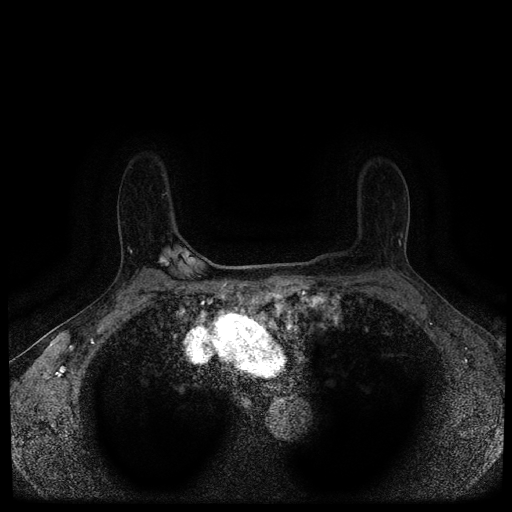
Breast MRI (dynamic contrast-enhanced, multi-phase), one axial slice. Position 77 of 116 along the scan axis. Dynamic contrast-enhanced series, time point 2 of 5 at this slice position (early post-contrast). 1.5 T. TE 2.7 ms, TR 5.4 ms. 512 × 512 image matrix, field of view 330 × 330 mm. Patient: female, 63 years.
Annotated regions visible in this slice (semi-automatic segmentation, software-assisted and operator-edited):
- breast lesion (labelled 'tumour' in the annotation; benign lesions carry a separate 'benign' label): bounding box [x1, y1, x2, y2] px = [157, 255, 170, 267]